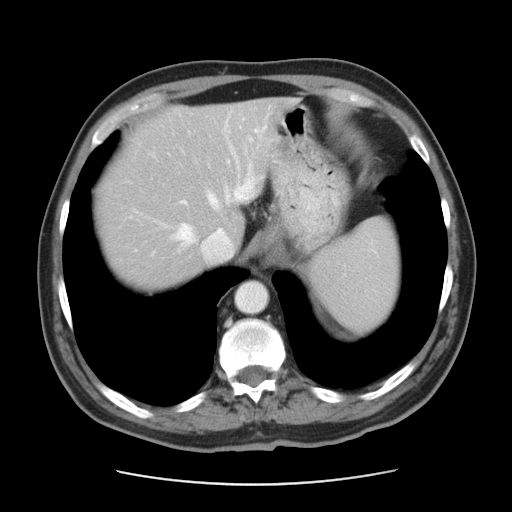
Contrast-enhanced abdominal CT, one axial slice; slice 35 of 42 in the series (ordered by position); 120 kVp; intravenous contrast given; soft-tissue window (W 400 / L 40 HU); 5 mm slice thickness; 512 × 512 image matrix, field of view 370 × 370 mm. Male patient, age 73 years. Case-level facts recorded for this patient, not image findings: diagnosis: colorectal cancer liver metastases, imaged before liver resection; multiple liver metastases: yes; largest metastasis: 0.5 cm; disease in both lobes: no.
Annotated regions visible in this slice (expert manual segmentation):
- hepatic veins: bounding box (x1, y1, x2, y2) in pixels: (153, 145, 255, 259)
- liver: (97, 99, 286, 286)
- planned liver remnant (the part of the liver to remain after resection): (131, 99, 287, 236)